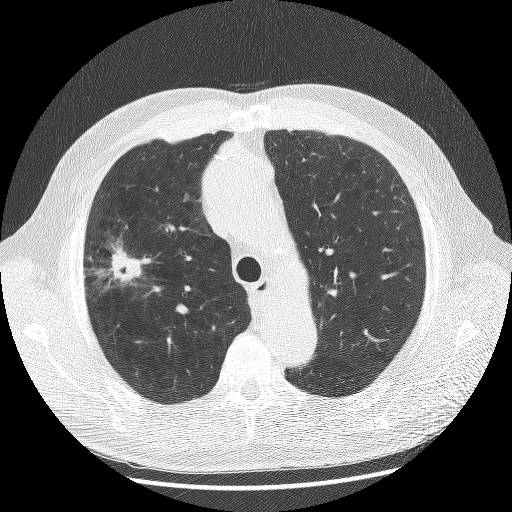
Chest CT (low-dose screening protocol), one axial image; baseline annual screen; lung window (W 1500 / L -600 HU); lung (sharp) reconstruction kernel (BONE); slice 42 of 175 in the series; 512 × 512 image matrix. Male participant, aged 70 years at enrolment.
Expert-annotated lung lesion, bounding box <77,235,148,306> (left, top, right, bottom; pixels). The screening reader recorded 2 non-calcified nodules or masses ≥4 mm on this exam (left upper lobe, right upper lobe); which of them this box marks is not recorded. Later outcome: lung cancer diagnosed 23 days after this screen — non-small cell carcinoma, right upper lobe, poorly differentiated (G3), stage IA (AJCC 6th edition), 20 mm at pathology.